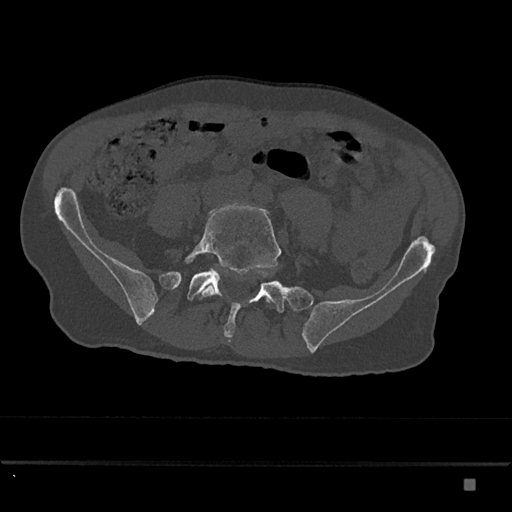
CT including the spine, one axial slice. Position 259 of 797 along the scan axis. Reconstruction kernel Br40s/3. Bone window (W 1800 / L 400 HU). 0.5 mm slice thickness. 512 × 512 image matrix, field of view 390 × 390 mm. Patient: male, 72 years. From the clinical record (not read from this slice): primary cancer: prostate.
Outlined on this slice (semi-automatically segmented with operator editing):
- L5 vertebra: bounding box (x1, y1, x2, y2) in pixels: (185, 204, 281, 303)